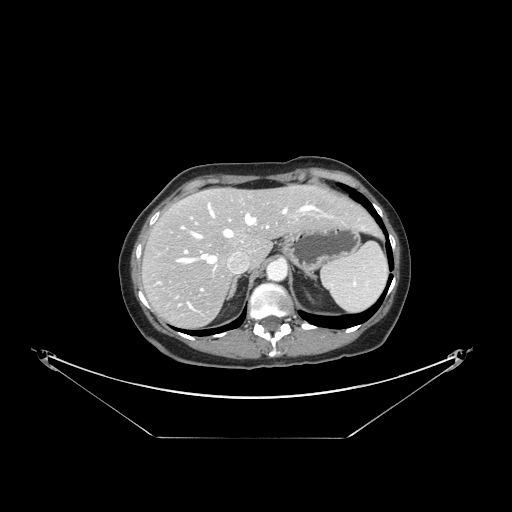
Contrast-enhanced abdominal CT, one axial slice; position 111 of 148 along the scan axis; soft-tissue window (W 400 / L 40 HU); 2.5 mm slice thickness; 512 × 512 image matrix, field of view 500 × 500 mm. Female patient, age 73 years. Case-level facts recorded for this patient, not image findings: diagnosis: colorectal cancer liver metastases, imaged before liver resection; multiple liver metastases: no; largest metastasis: 1 cm; disease in both lobes: no.
Structures marked on this image (outlined manually by an expert reader):
- hepatic veins: bounding box <175,203,316,309> (left, top, right, bottom; pixels)
- liver: <144,186,377,327>
- planned liver remnant (the part of the liver to remain after resection): <168,186,377,263>
- portal vein (with intrahepatic branches): <184,210,331,291>